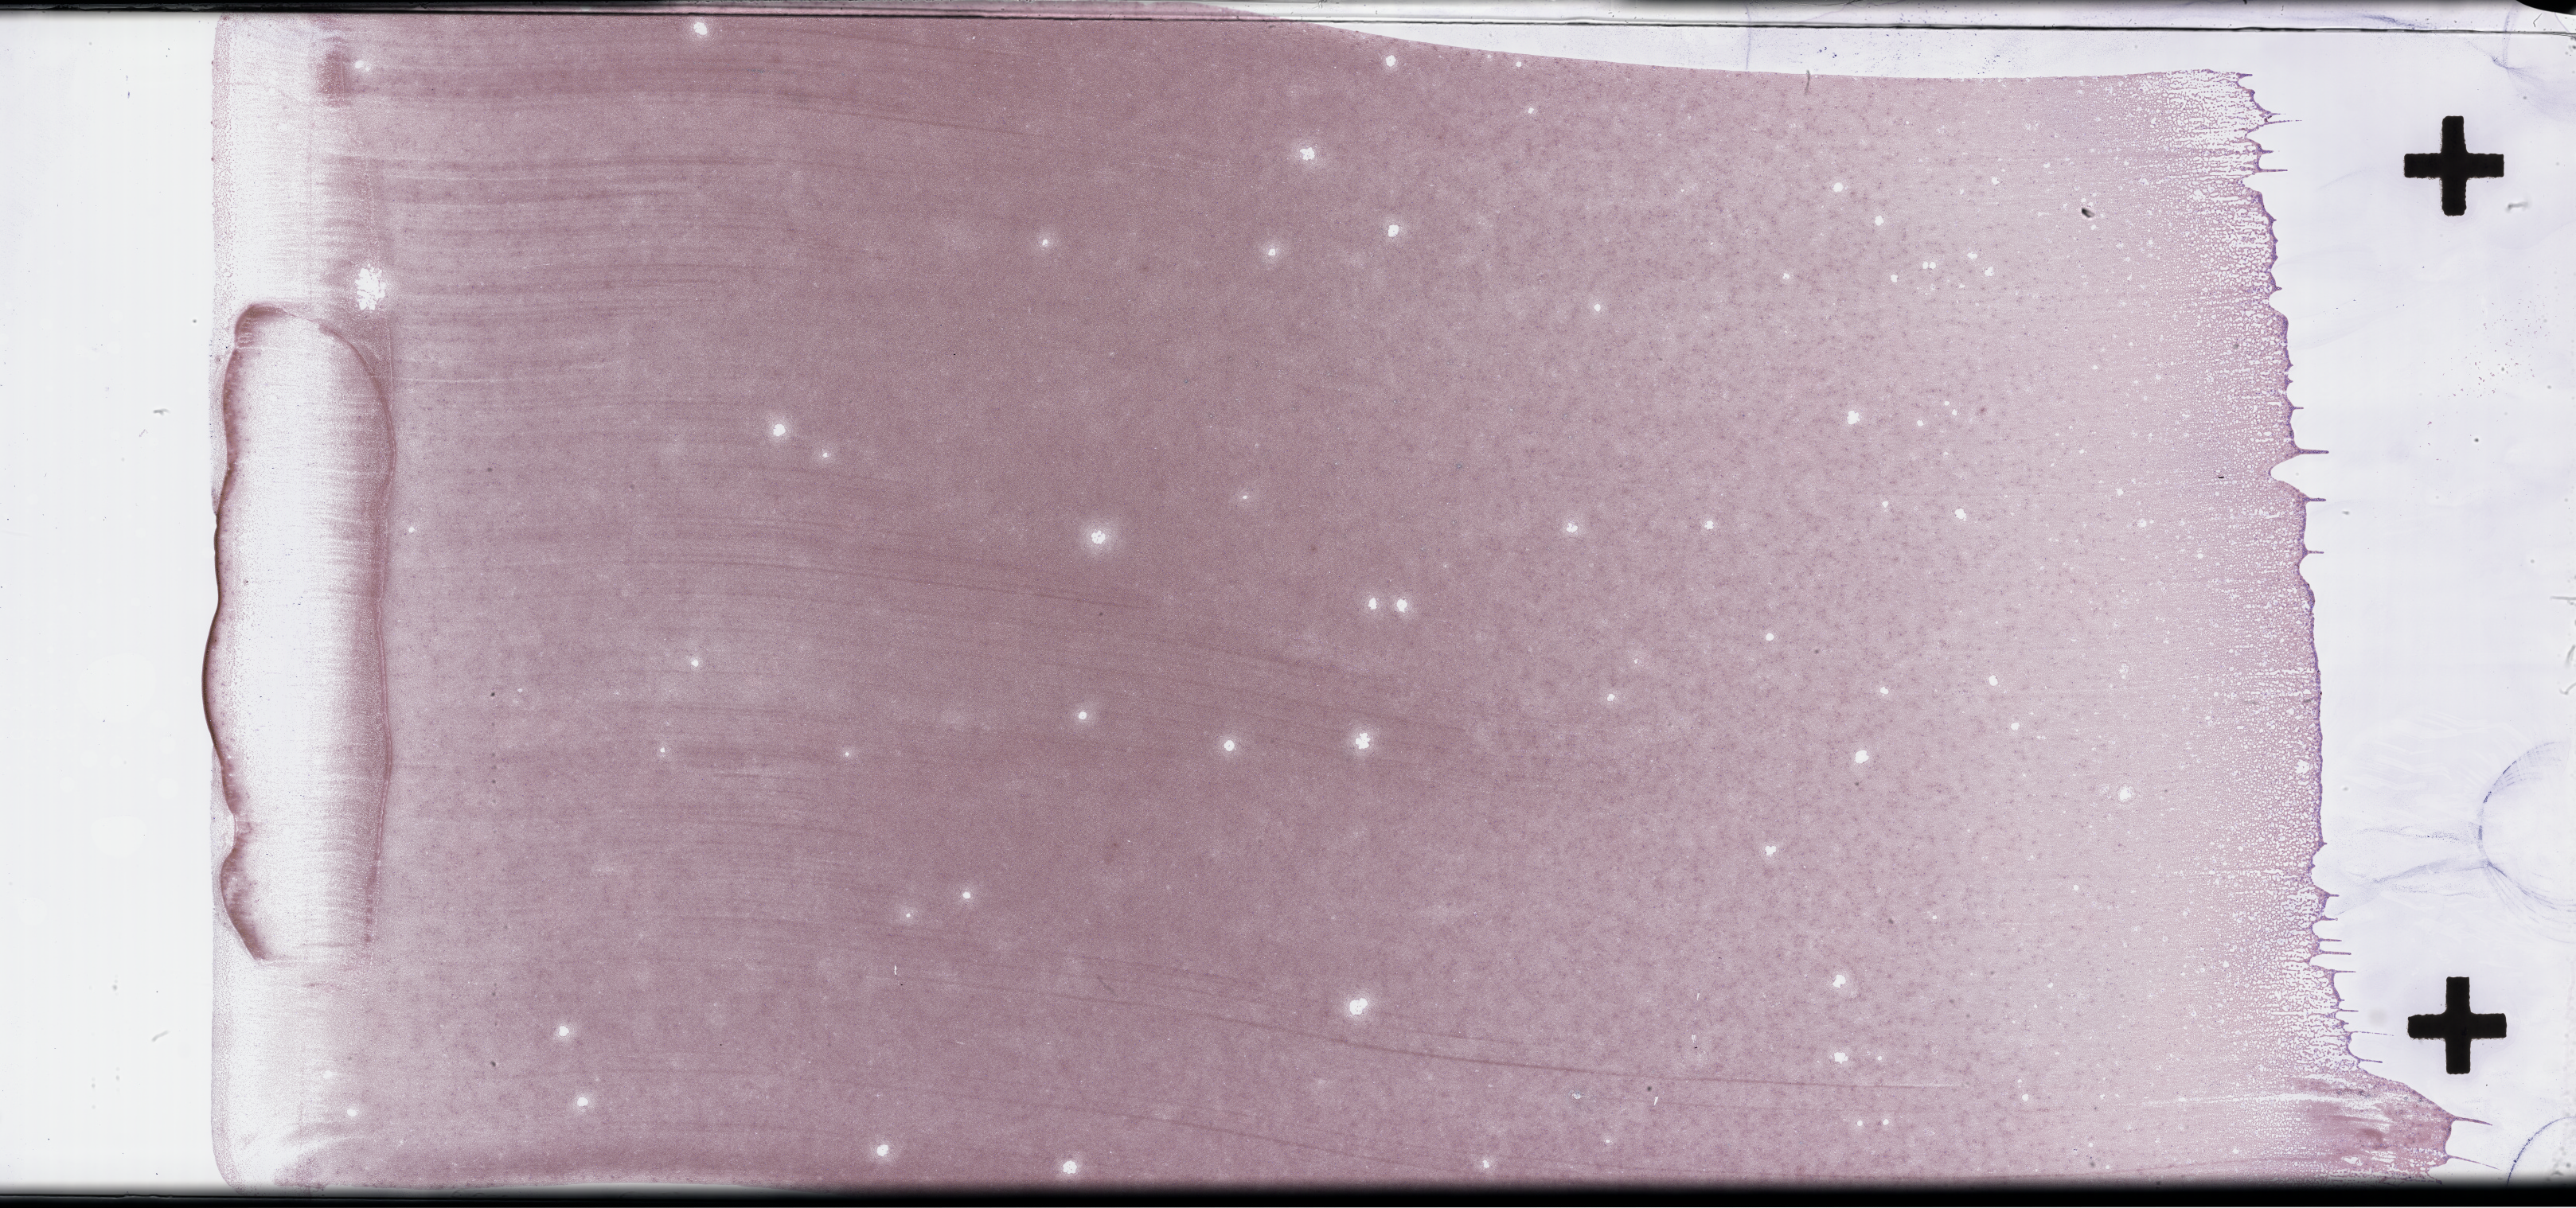
Wright-Giemsa-stained bone marrow smear, whole-slide image, shown as a low-resolution overview of the whole scanned area (about 52.3 x 24.5 mm), collected at baseline (before treatment). Patient sex: female.
From a patient with: Plasma Cell Myeloma.